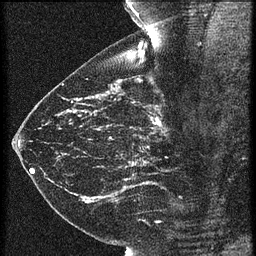
Breast MRI (dynamic contrast-enhanced), one sagittal slice; slice 34 of 60 in the series (ordered by position); 3 images stored at this slice position (order not interpretable as contrast timing); 1.5 T; TE 4.2 ms, TR 21.3 ms; 256 × 256 image matrix, field of view 180 × 180 mm. Patient: female, 43 years. From the clinical record (not read from this slice): setting: breast cancer imaged before/during neoadjuvant chemotherapy; receptor status: HER2-positive.
Annotated regions visible in this slice (semi-automatically segmented with operator editing):
- analysis volume of interest (the breast-tissue region the enhancement analysis was run in; not a lesion): bounding box <119,114,189,173> (left, top, right, bottom; pixels)
- tumour enhancement mask (voxels above the 90 % enhancement threshold inside the analysis volume of interest): <131,114,161,165>